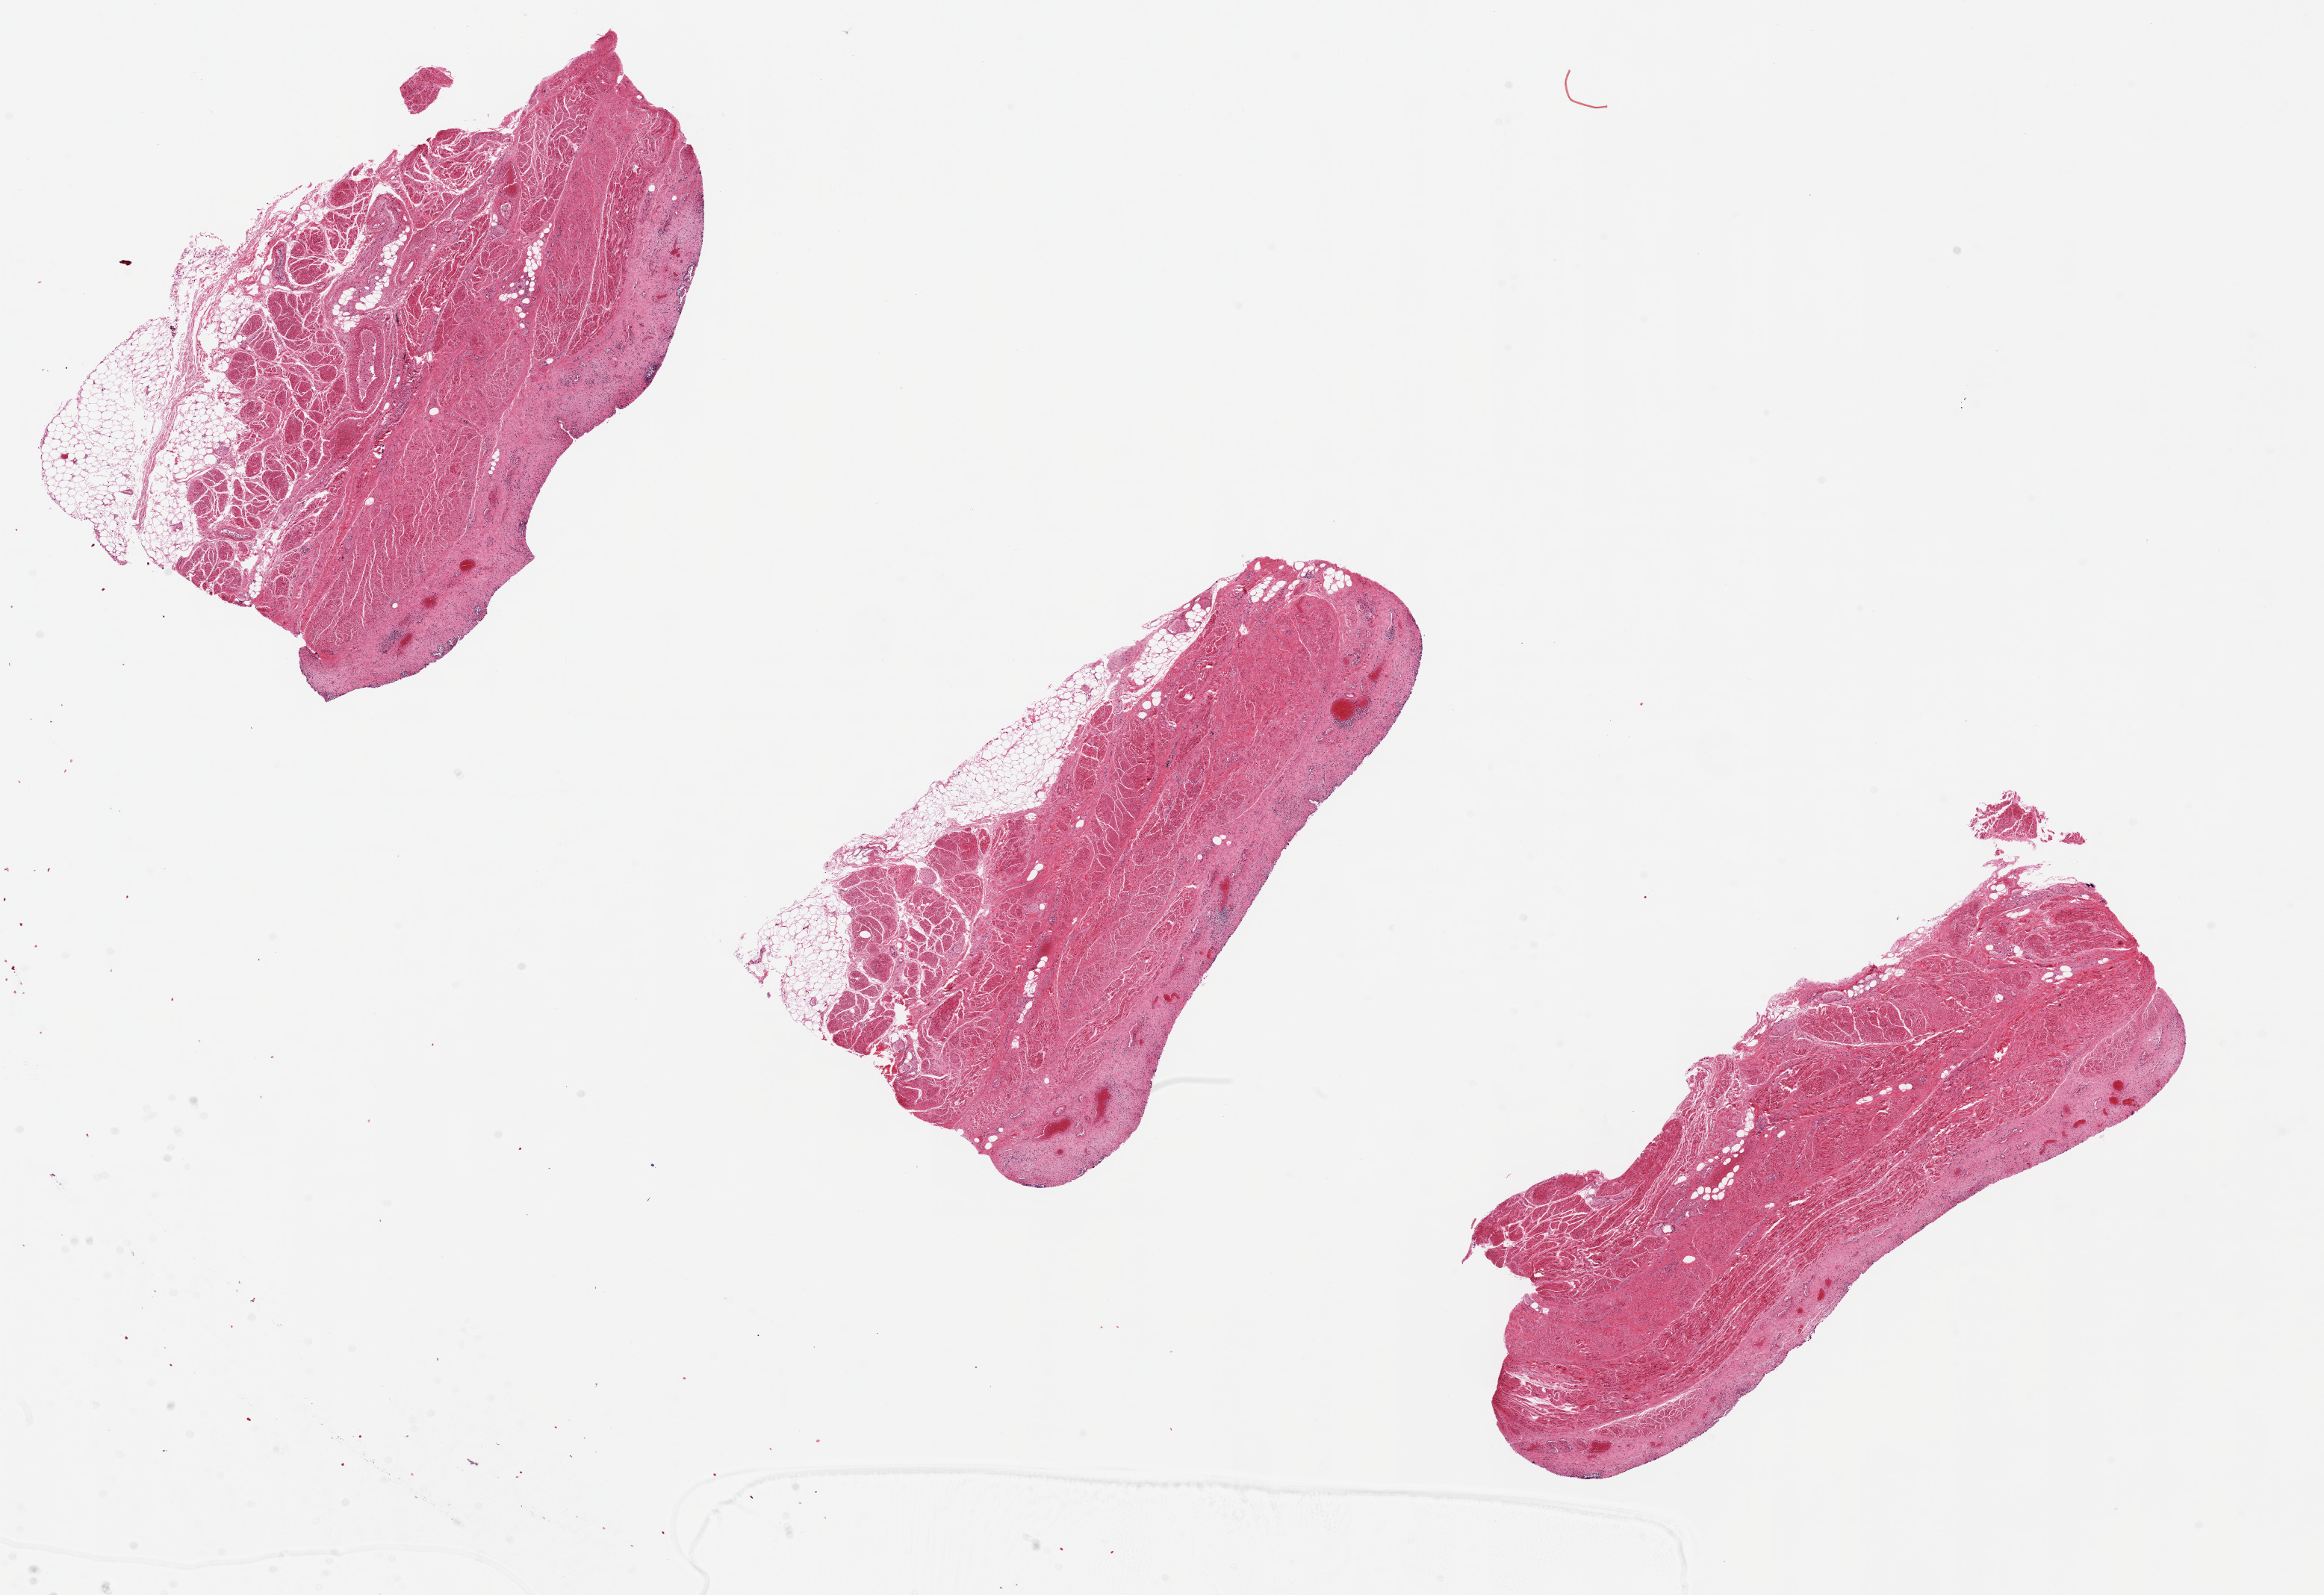
Digitized H&E-stained section, a low-resolution overview of the entire scanned area, about 24.6 x 16.9 mm. PAXgene-fixed paraffin-embedded (PFPE) section. Section of urinary bladder (target tissue). Tissue donor sample. Donor sex: female.
Reviewer comment on this tissue sample: Epithelium, 1. Wall. Three pieces.